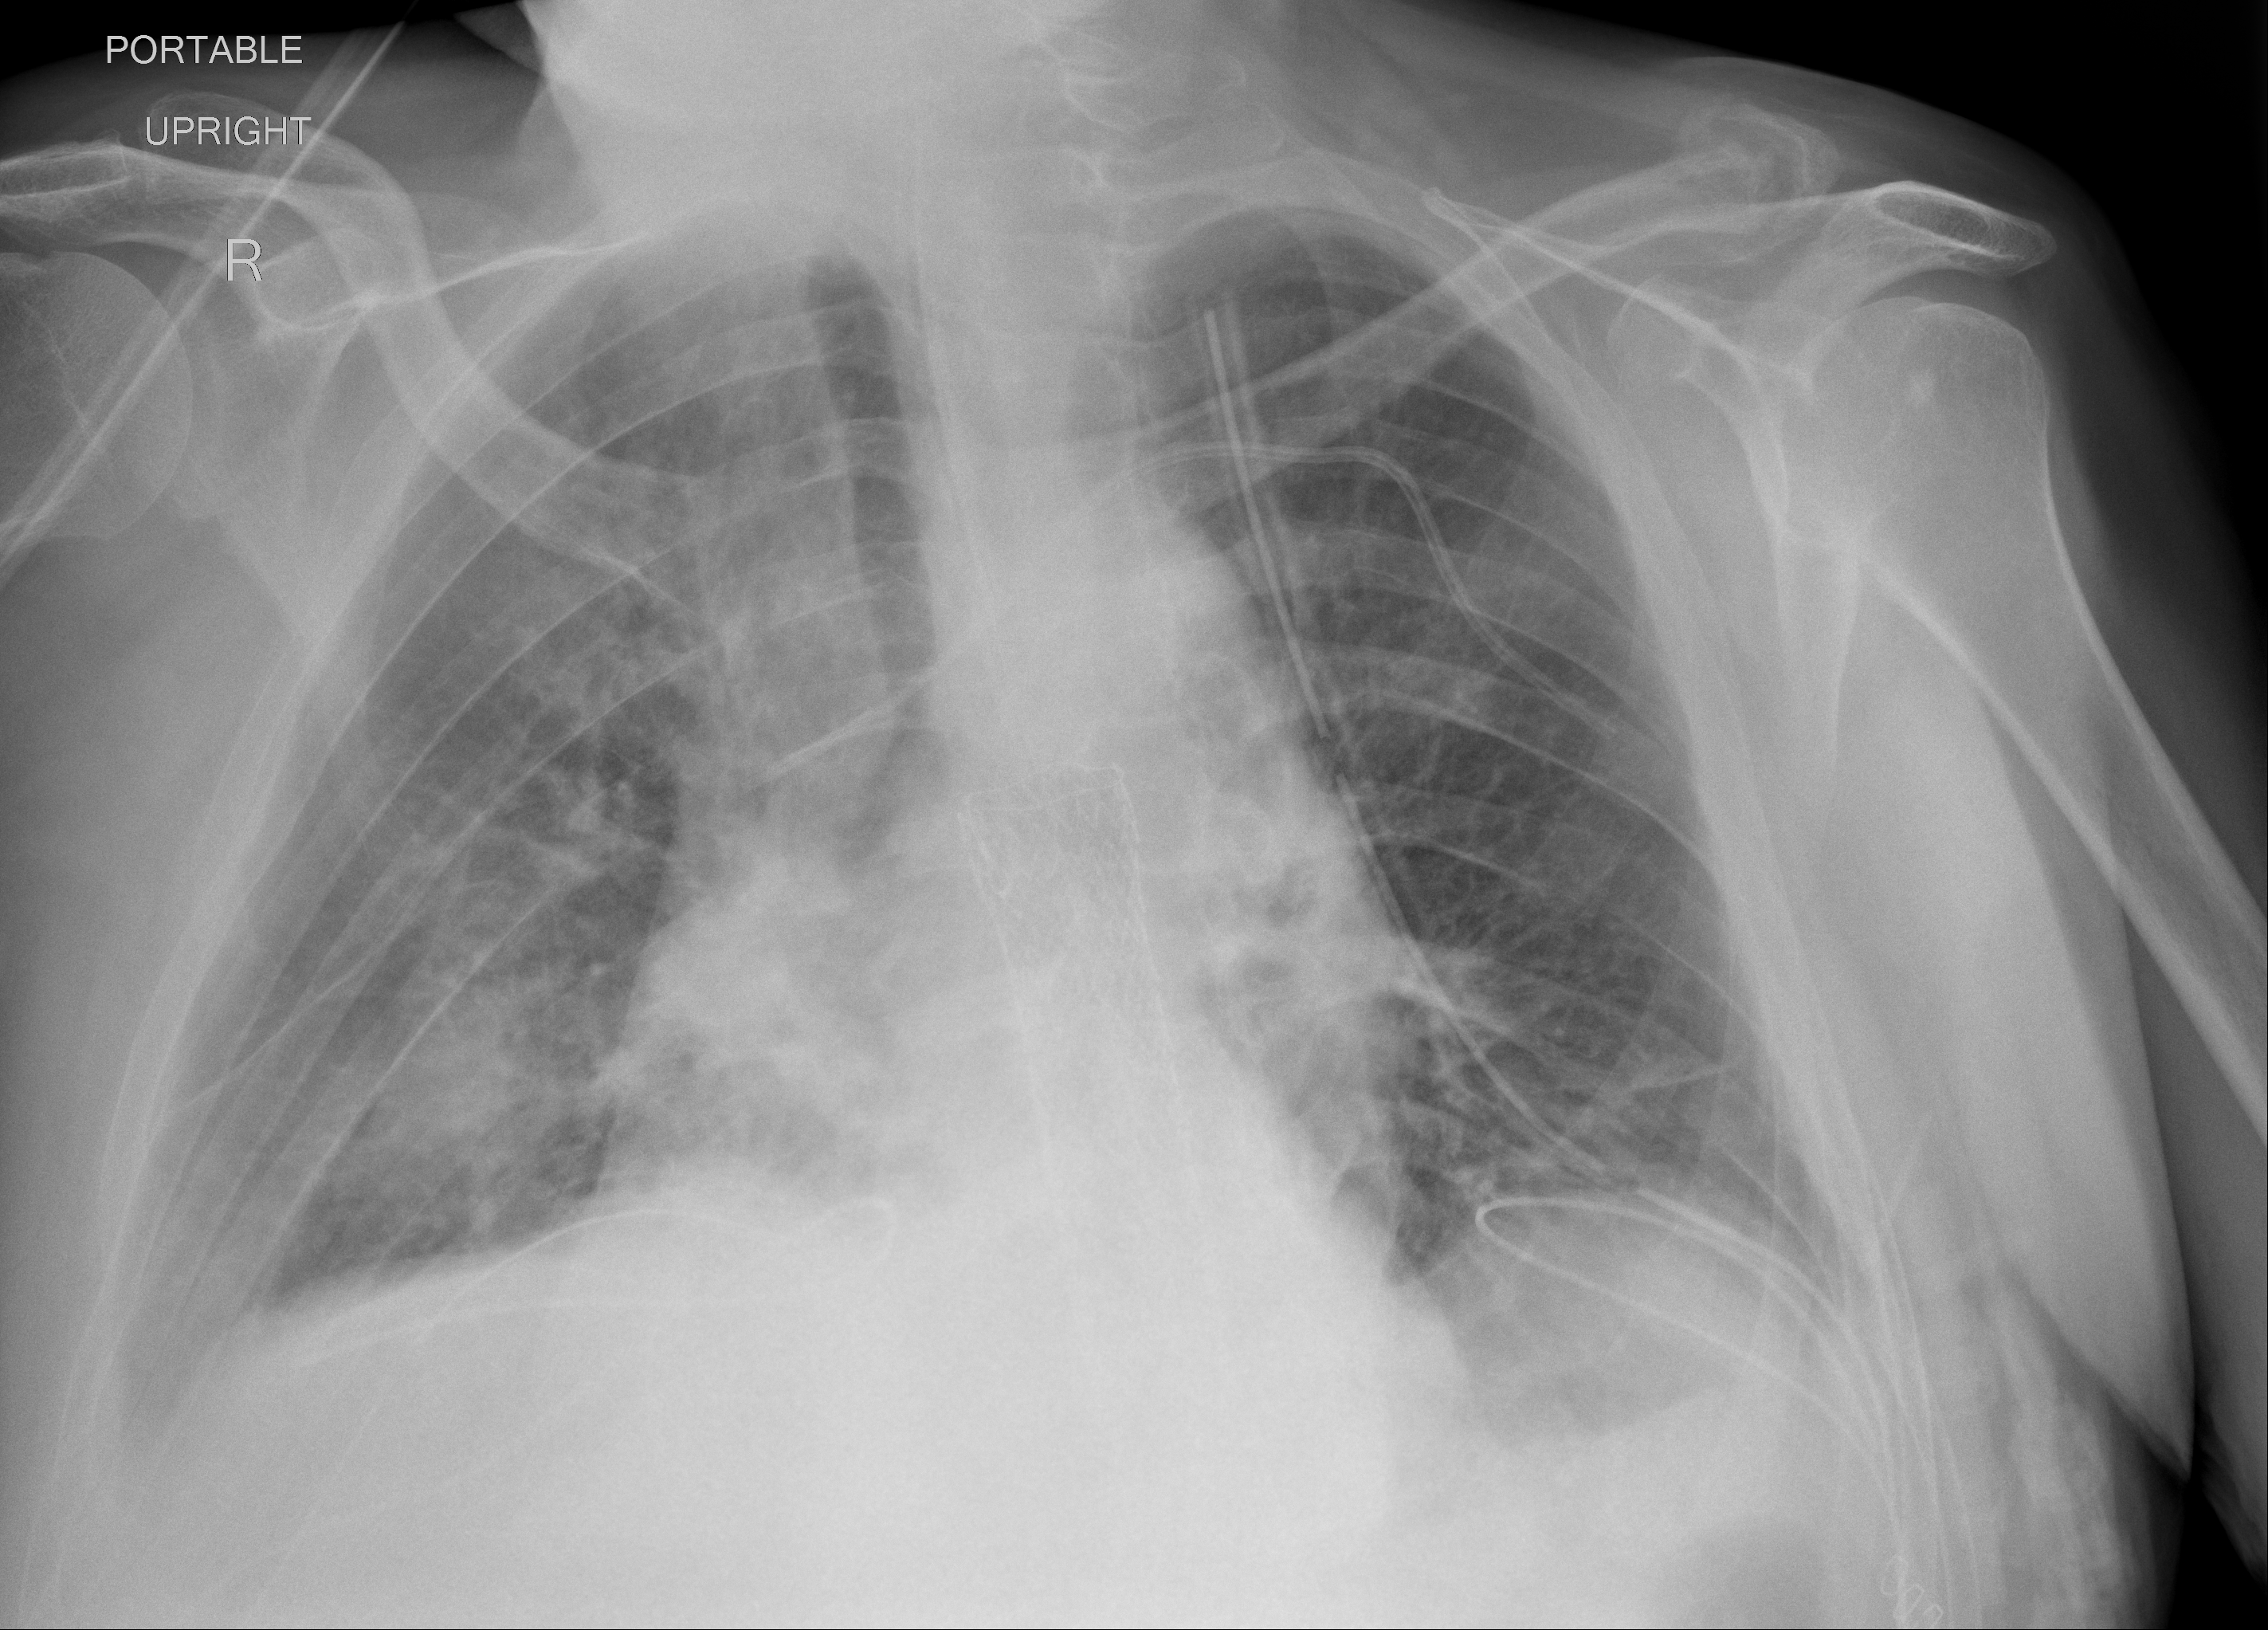
Portable chest radiograph, AP projection. Male patient, age 64 years; imaged 7 days after the COVID-19 diagnosis.
Radiologist key findings (as recorded): Mildly worsened right lung base airspace opacity. Unchanged left lung base atelectasis.